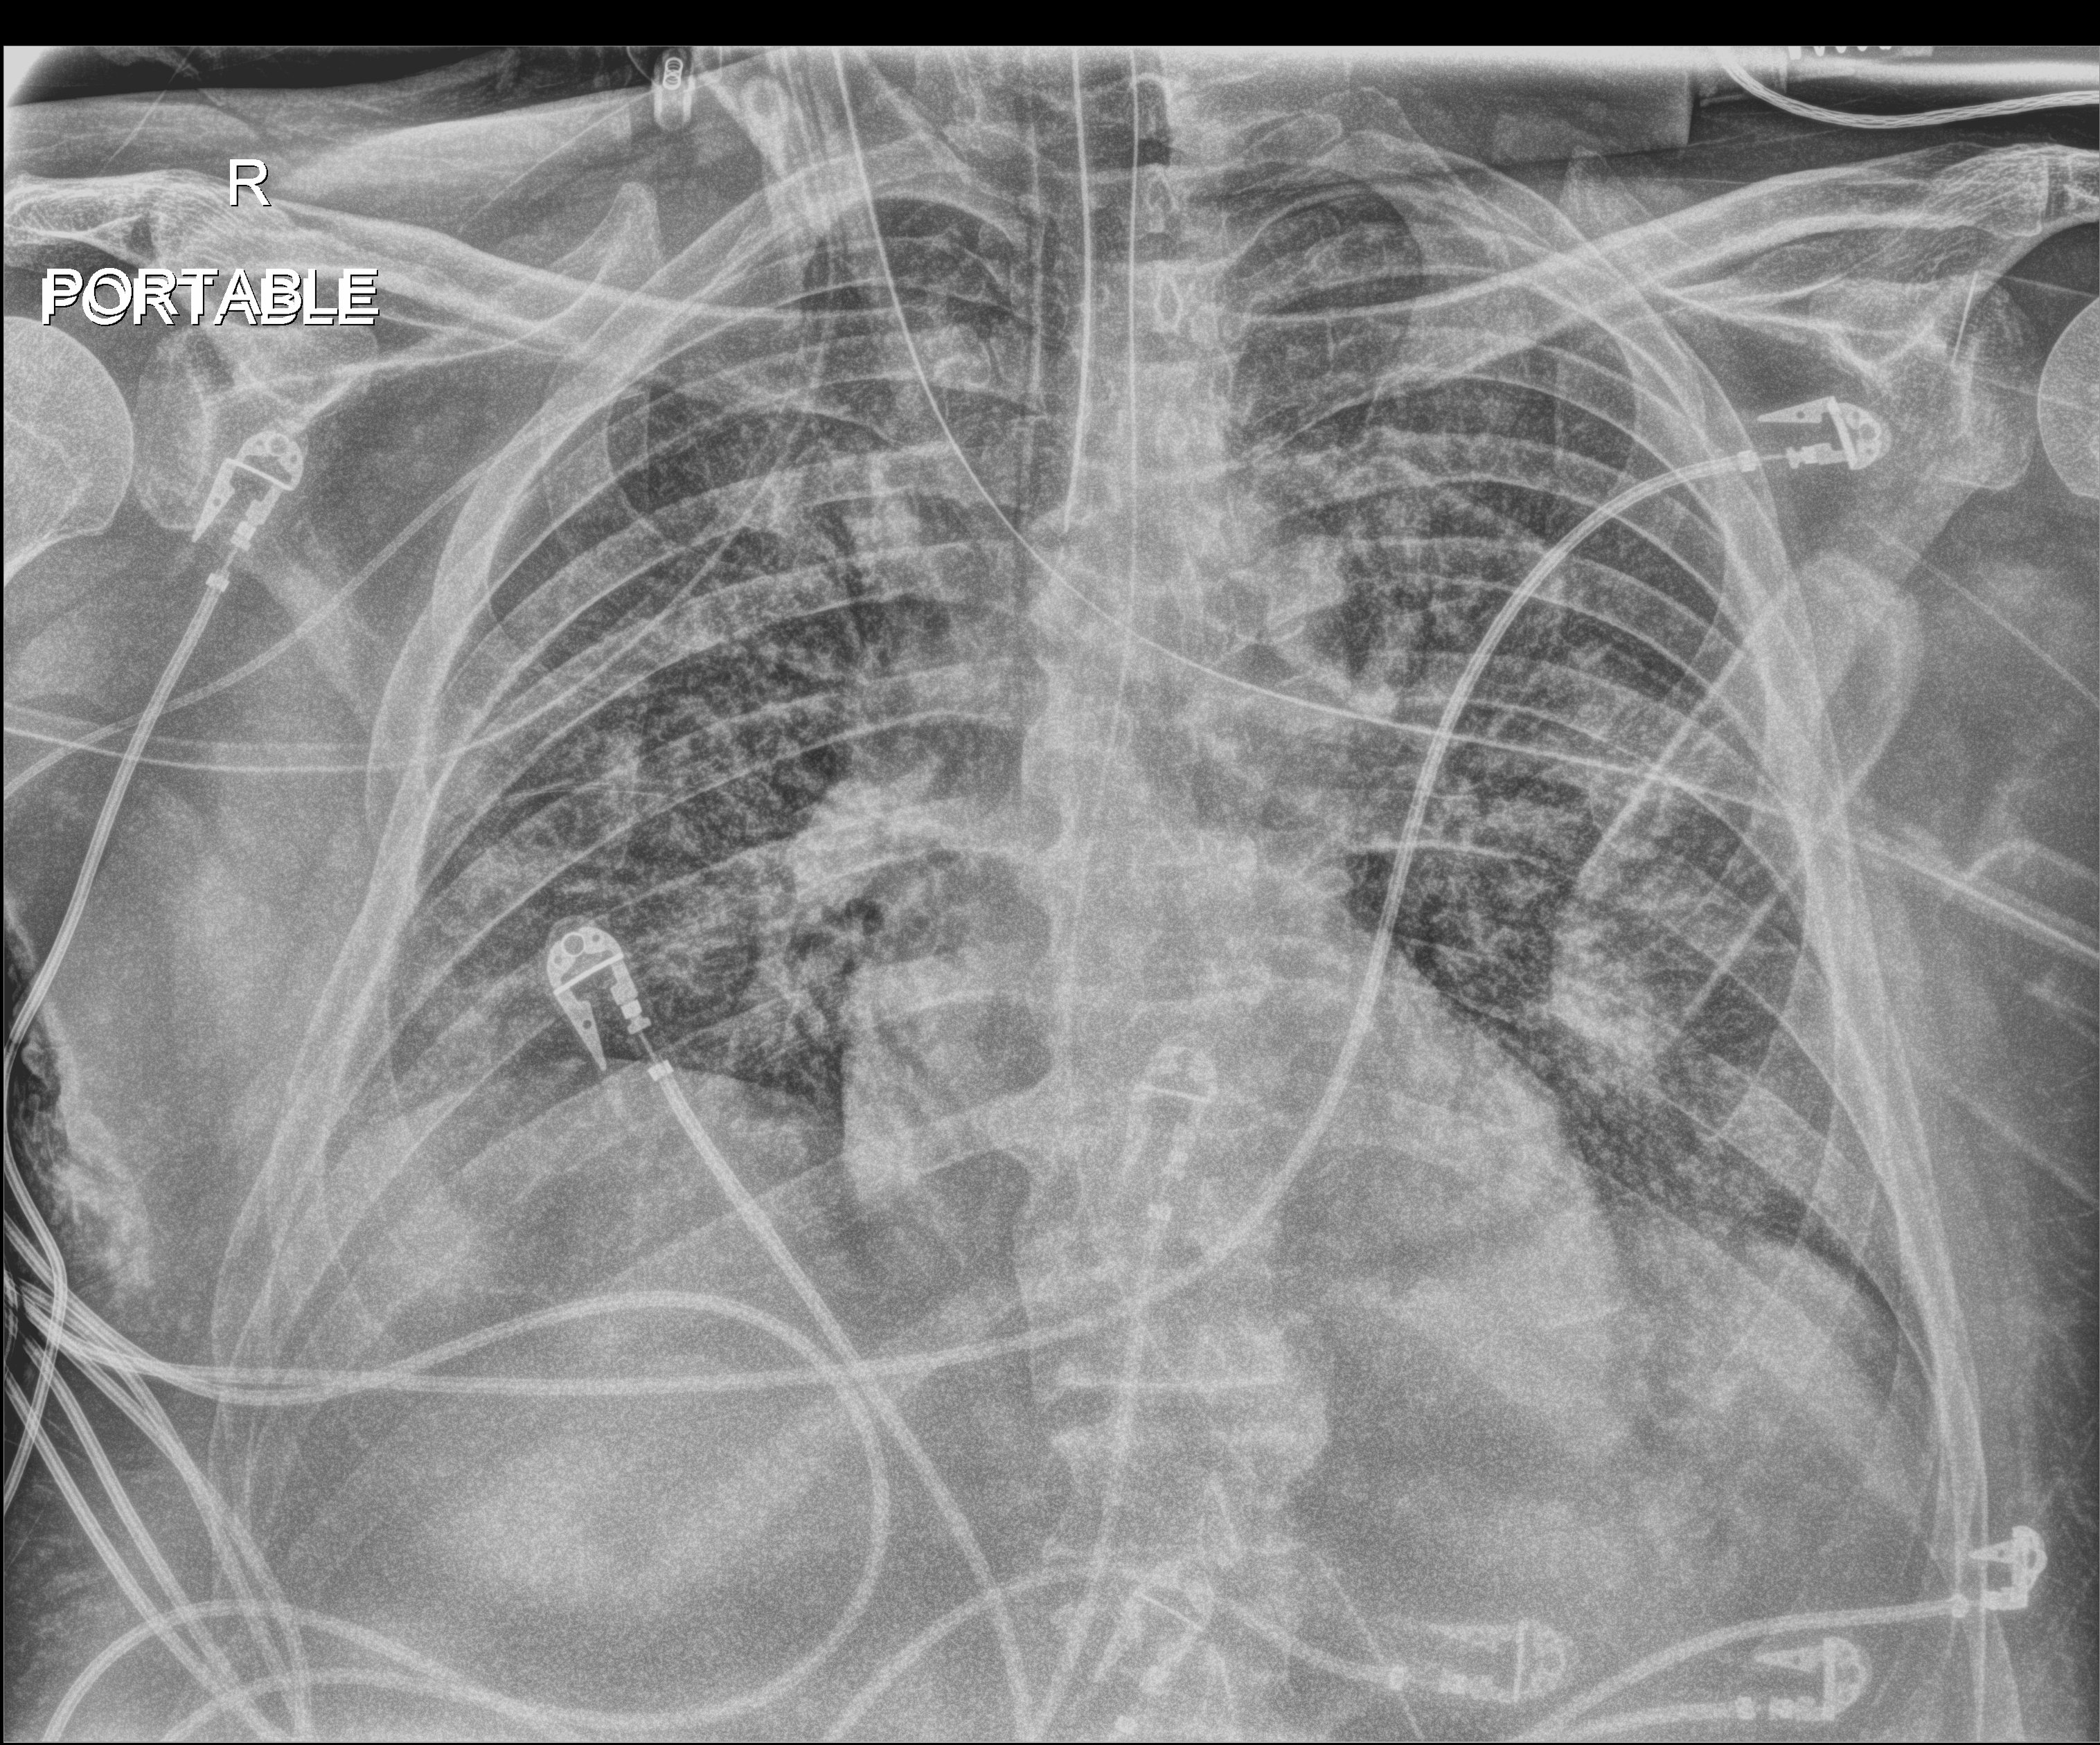
Bedside chest radiograph (digital radiography); anteroposterior (AP) projection. Male patient hospitalised with COVID-19, age 60–74 years.
Admission-level facts for this patient (not findings on this image; timing relative to this image not recorded): admitted to intensive care during this hospital stay: yes.